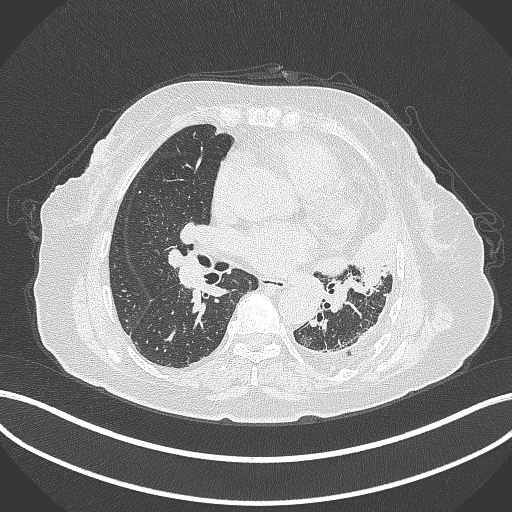
Chest CT, one axial slice; position 182 of 399 along the scan axis; 120 kVp; lung window (W 1500 / L -600 HU); 512 × 512 image matrix, field of view 400 × 400 mm. Female patient, age 75 years. From the clinical record (not read from this slice): clinical TNM (as recorded): T3 N3 M1.
Annotated regions visible in this slice (rectangle marked by the reading radiologist):
- lung tumour (recorded histology: adenocarcinoma): bounding box [x1, y1, x2, y2] px = [316, 218, 400, 282]